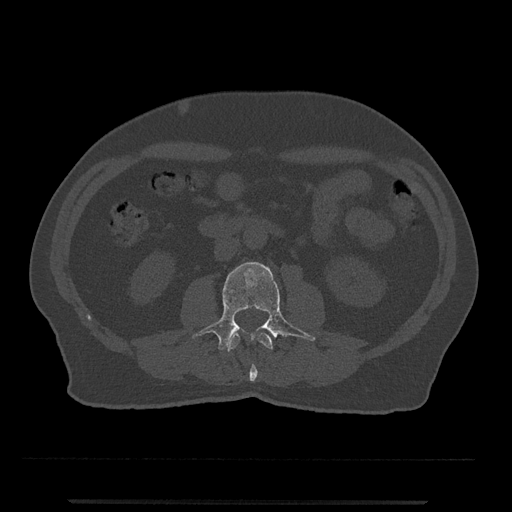
CT including the spine, one axial slice; reconstruction kernel Br40s/3; bone window (W 1800 / L 400 HU); 0.5 mm slice thickness; 512 × 512 image matrix, field of view 419 × 419 mm. Male patient, age 63 years. From the clinical record (not read from this slice): primary cancer: prostate.
Annotated regions visible in this slice (semi-automatically segmented with operator editing):
- L2 vertebra: bounding box <227,333,273,382> (left, top, right, bottom; pixels)
- L3 vertebra: <193,262,315,351>